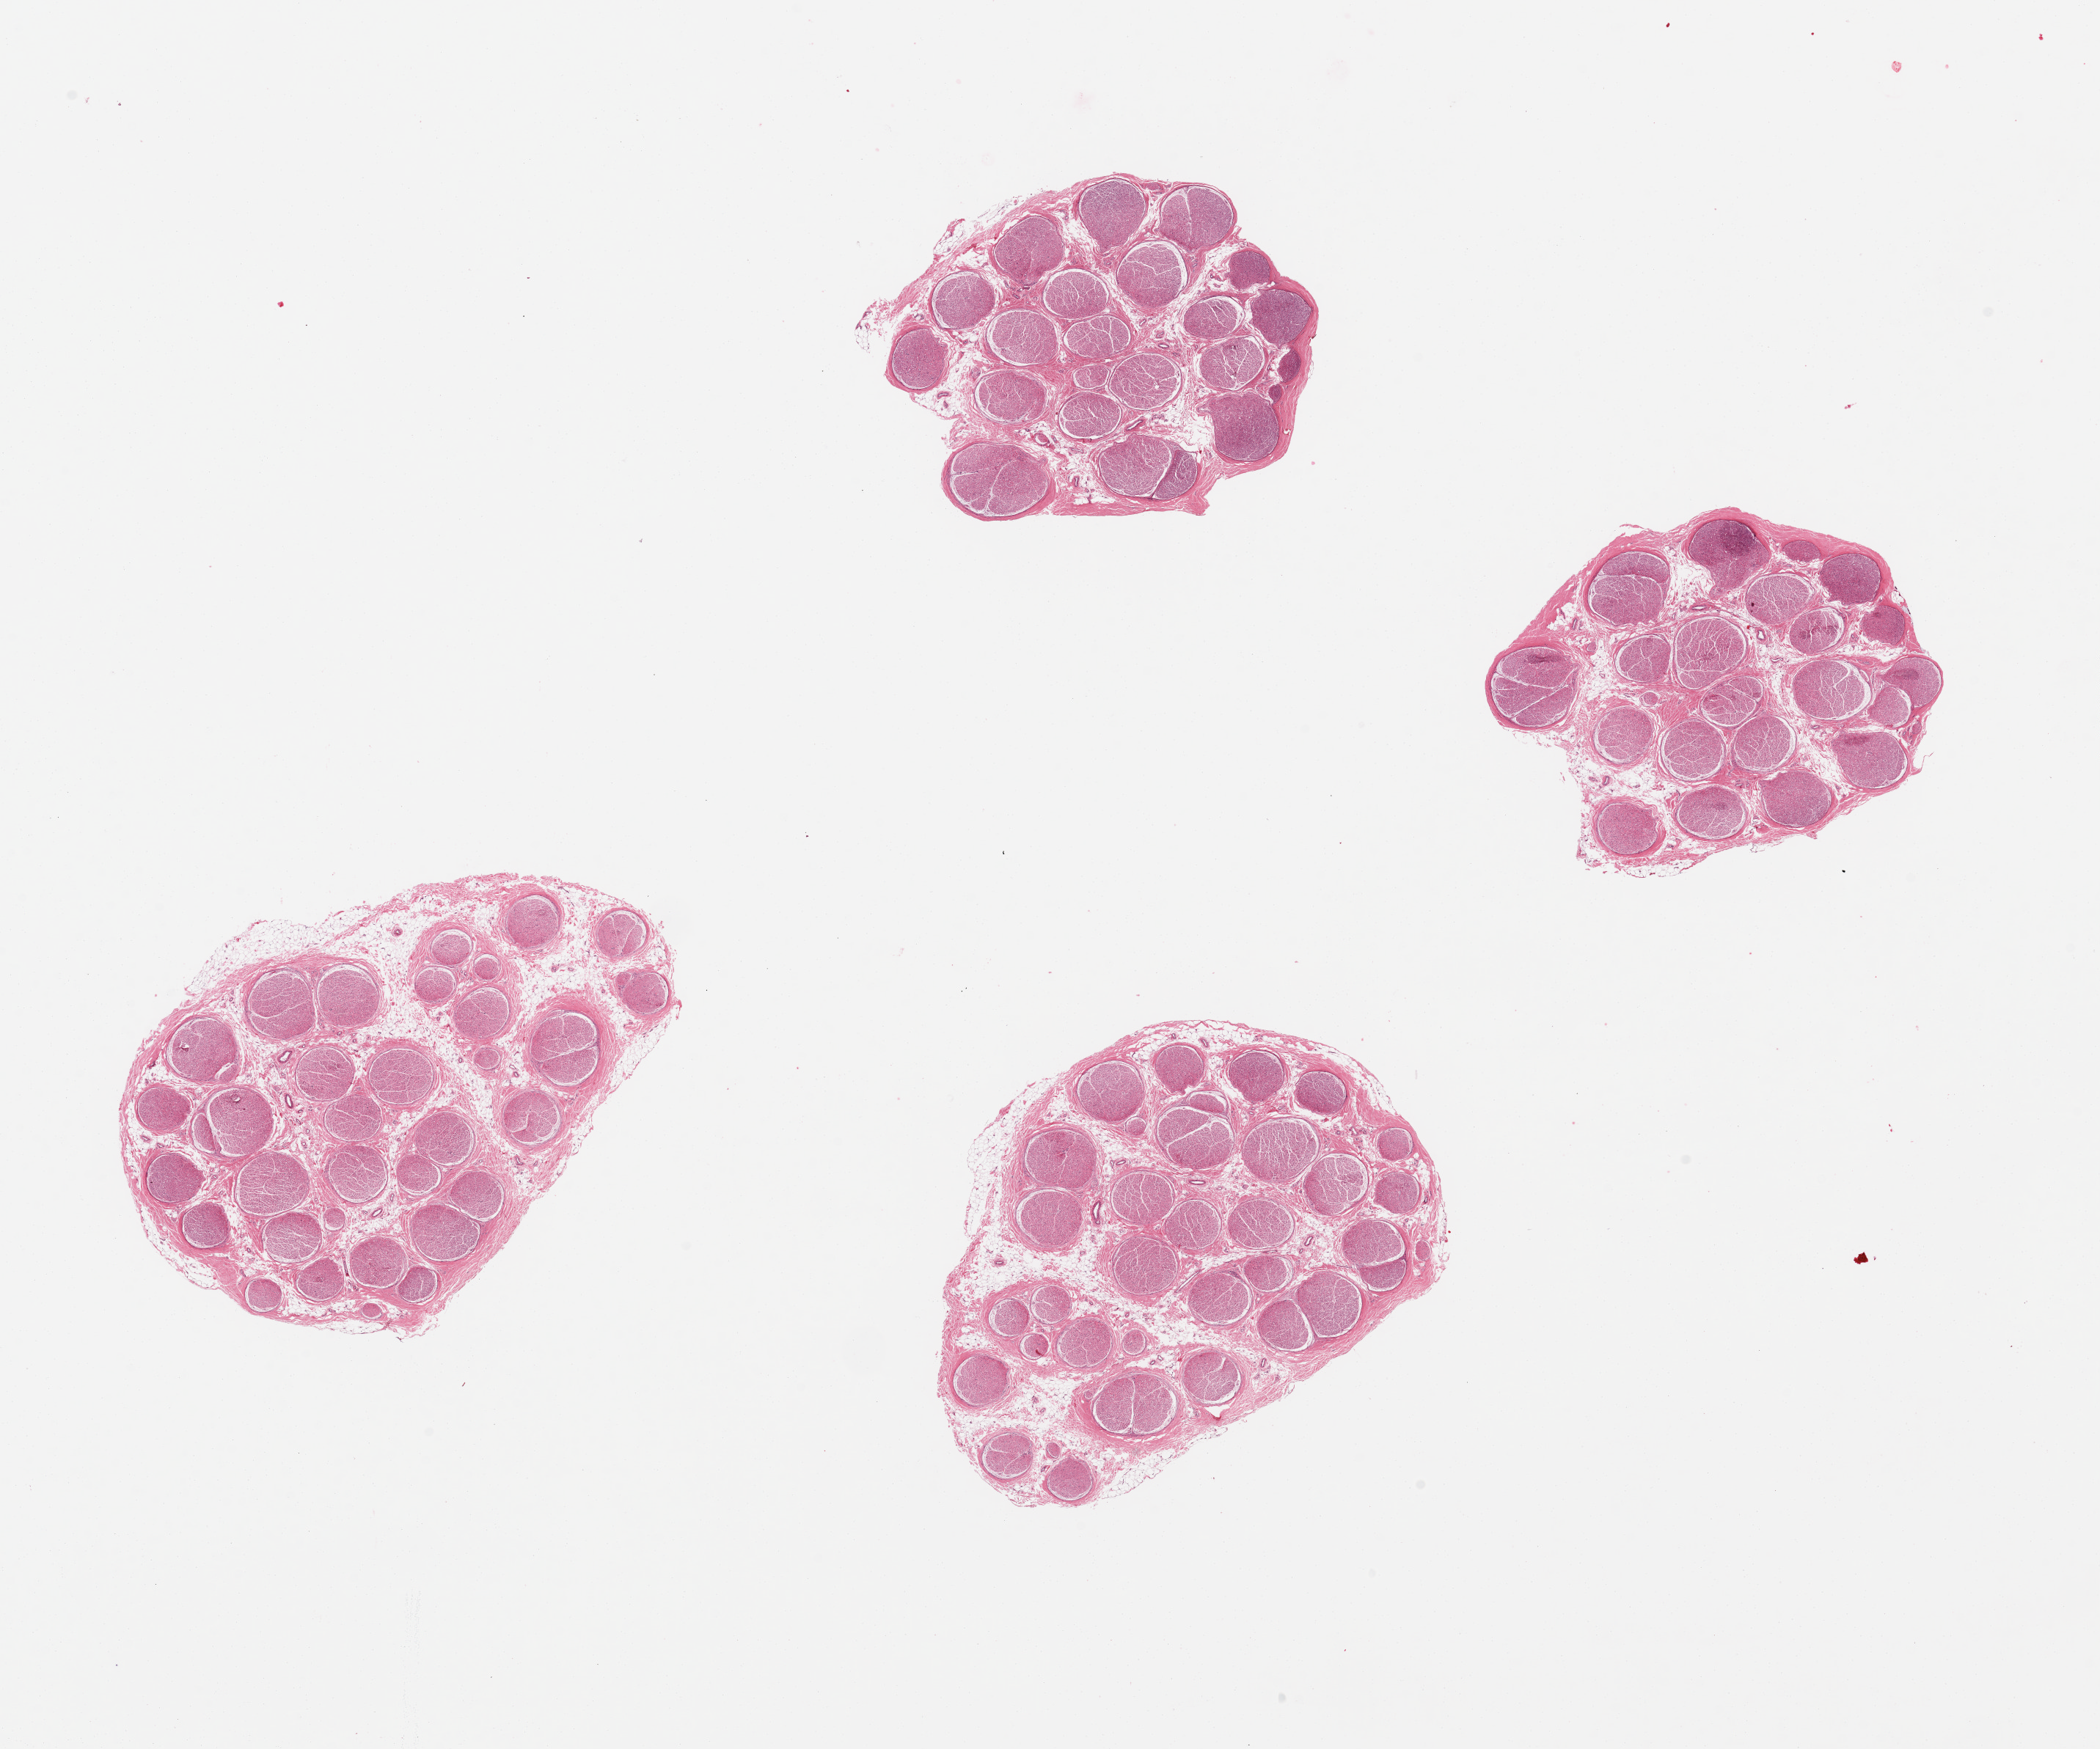
Whole-slide image, H&E stain, brightfield, low-resolution overview of the scanned area, about 22.6 x 18.9 mm (from a 20x scan). PAXgene-fixed paraffin-embedded (PFPE) section. Target tissue: tibial nerve. Donor tissue sample. Donor: female.
Reviewer comment on this tissue sample: 4 pieces, no adherent fat, good clean specimens.